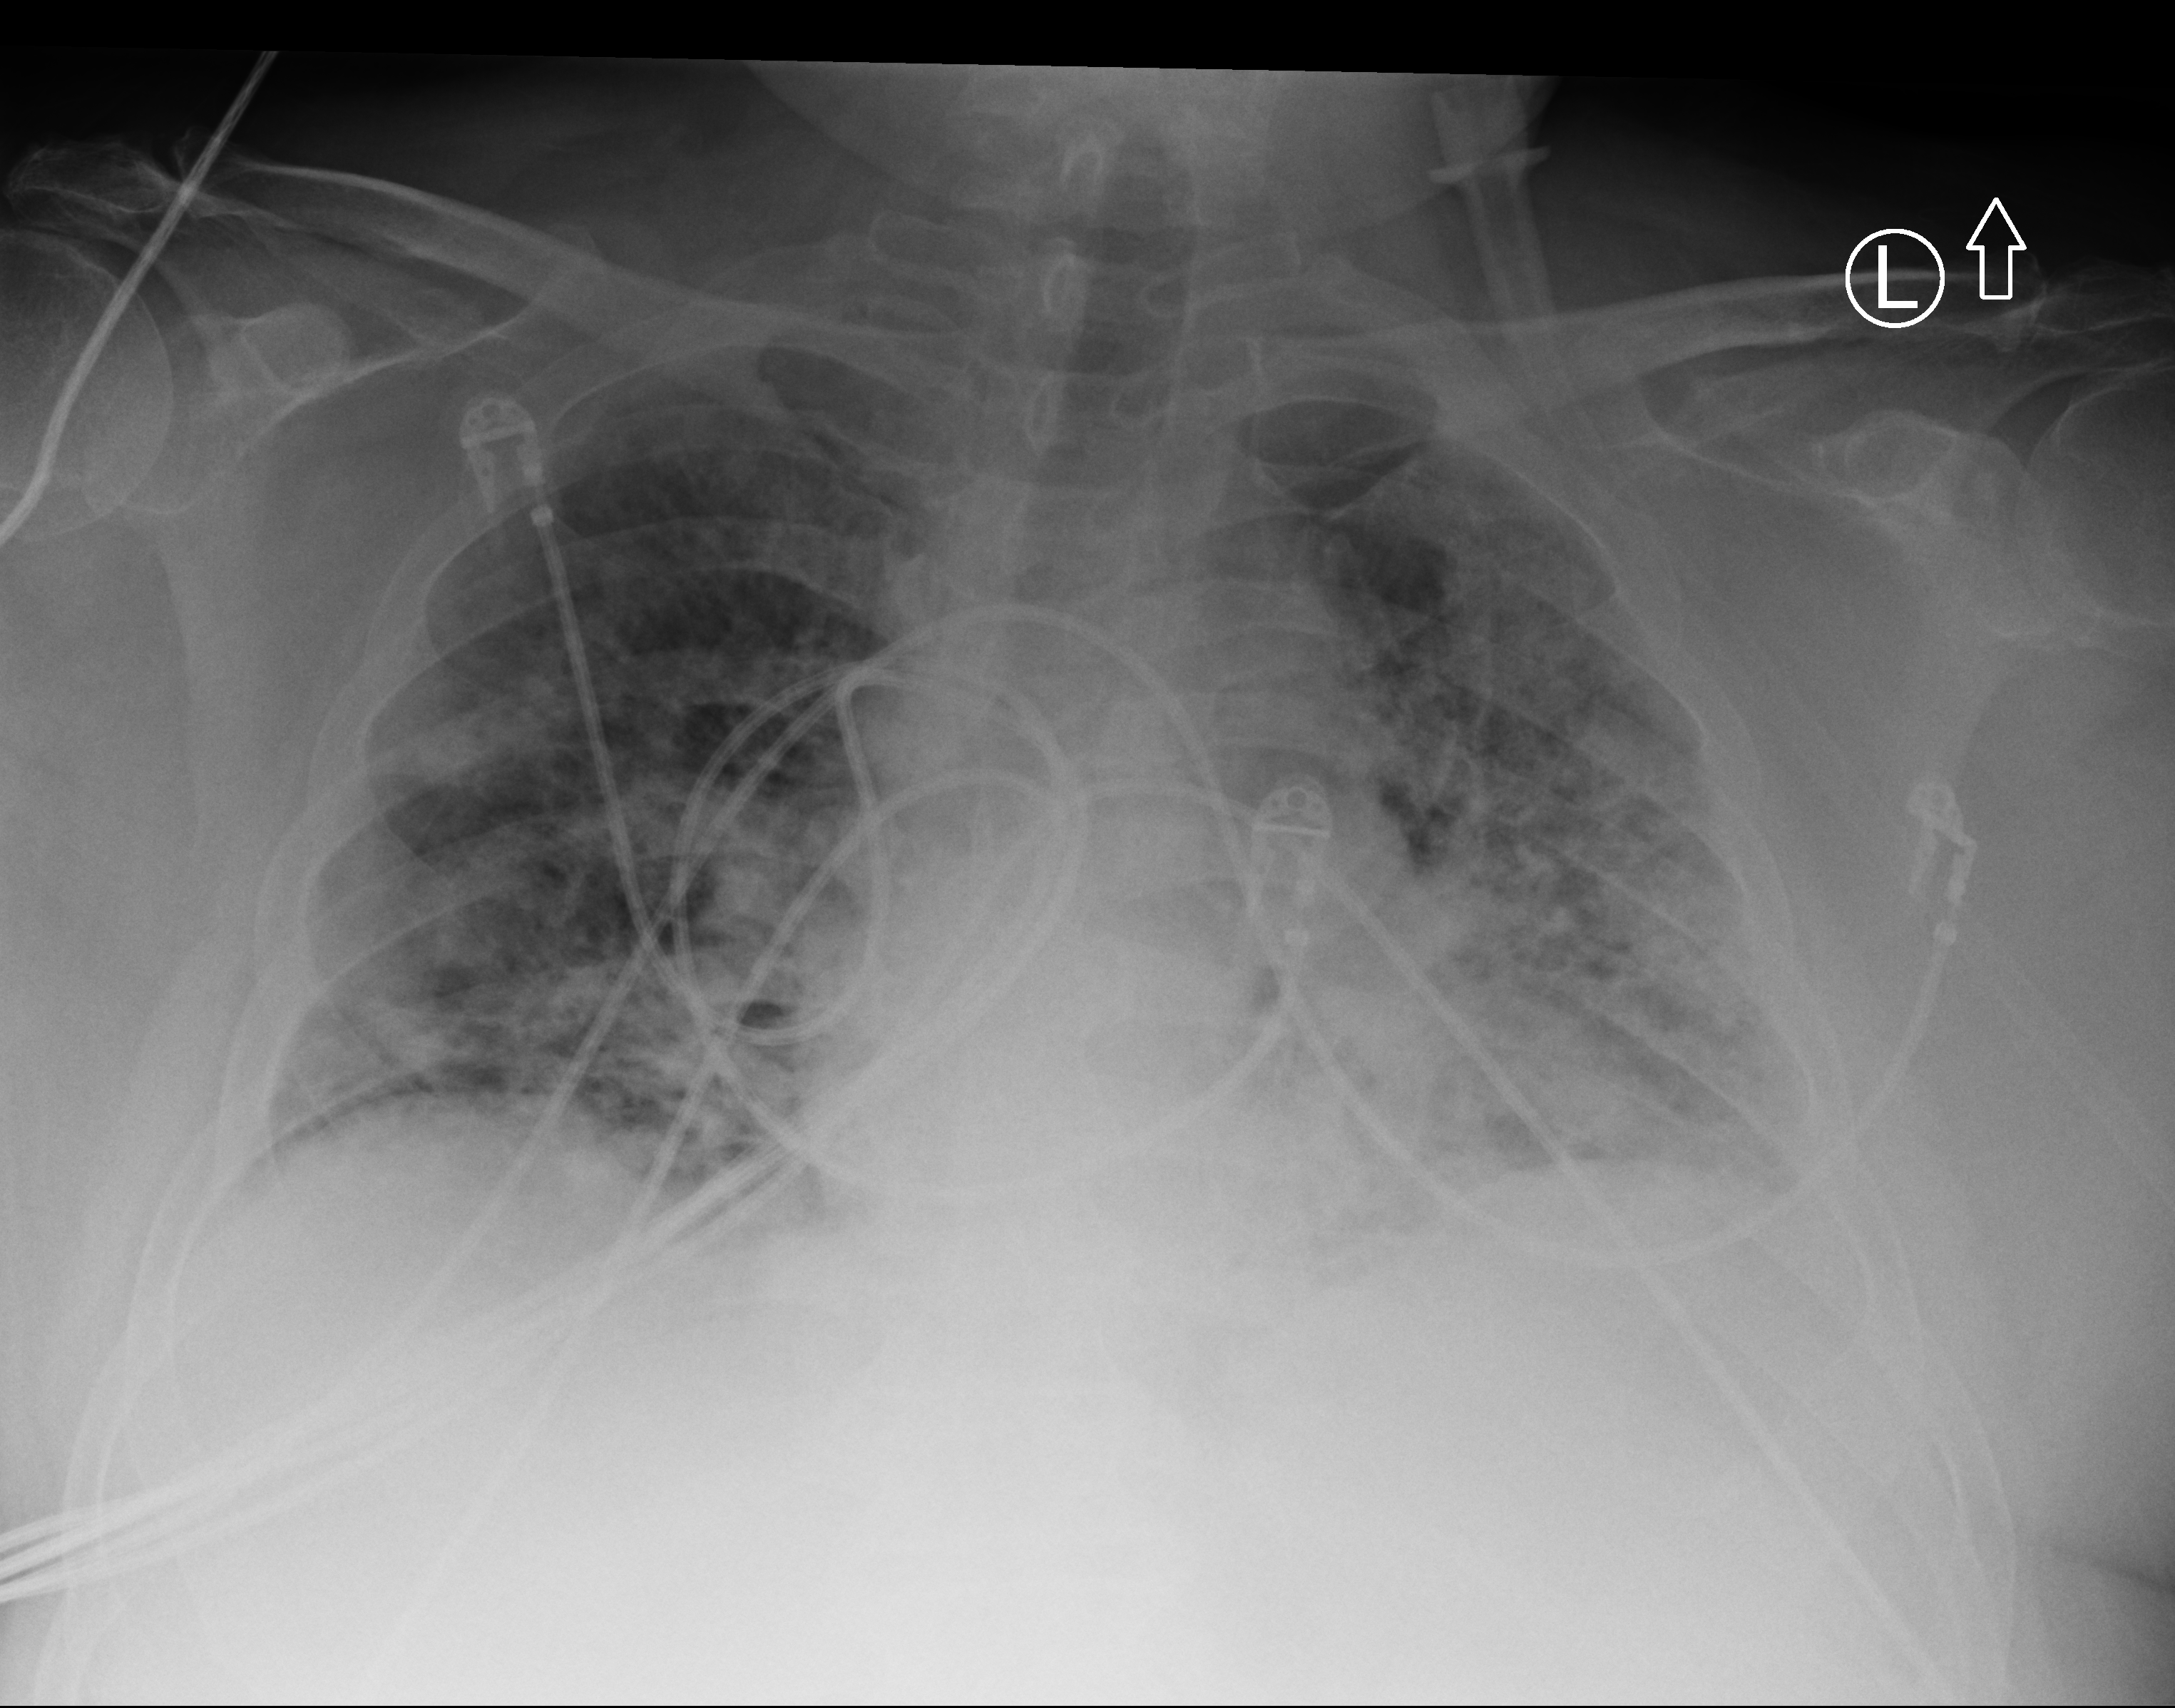
Portable chest radiograph. Male patient hospitalised with COVID-19, age 18–59 years.
From the hospital-stay record, not from the radiograph (when in the stay this image was taken is not recorded): mechanically ventilated during this hospital stay: no.